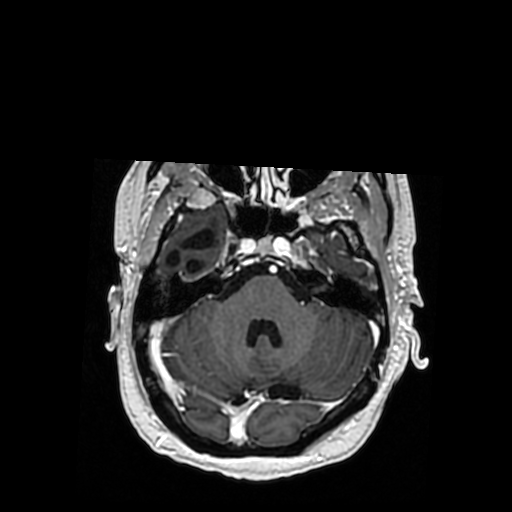
Brain MRI from a brain-tumour surgery series, one axial slice. Position 253 of 364 along the scan axis. T1-weighted post-contrast. 0.5 mm slice thickness. 512 × 512 image matrix. From the clinical record (not read from this slice): histopathology: Oligodendroglioma; WHO grade: 3; IDH mutation: yes; tumour location: Right Posterior Temporal Inferior Parietal.
Structures marked on this image (outlined manually by an expert reader):
- previous resection cavity: bounding box [x1, y1, x2, y2] px = [165, 229, 216, 273]